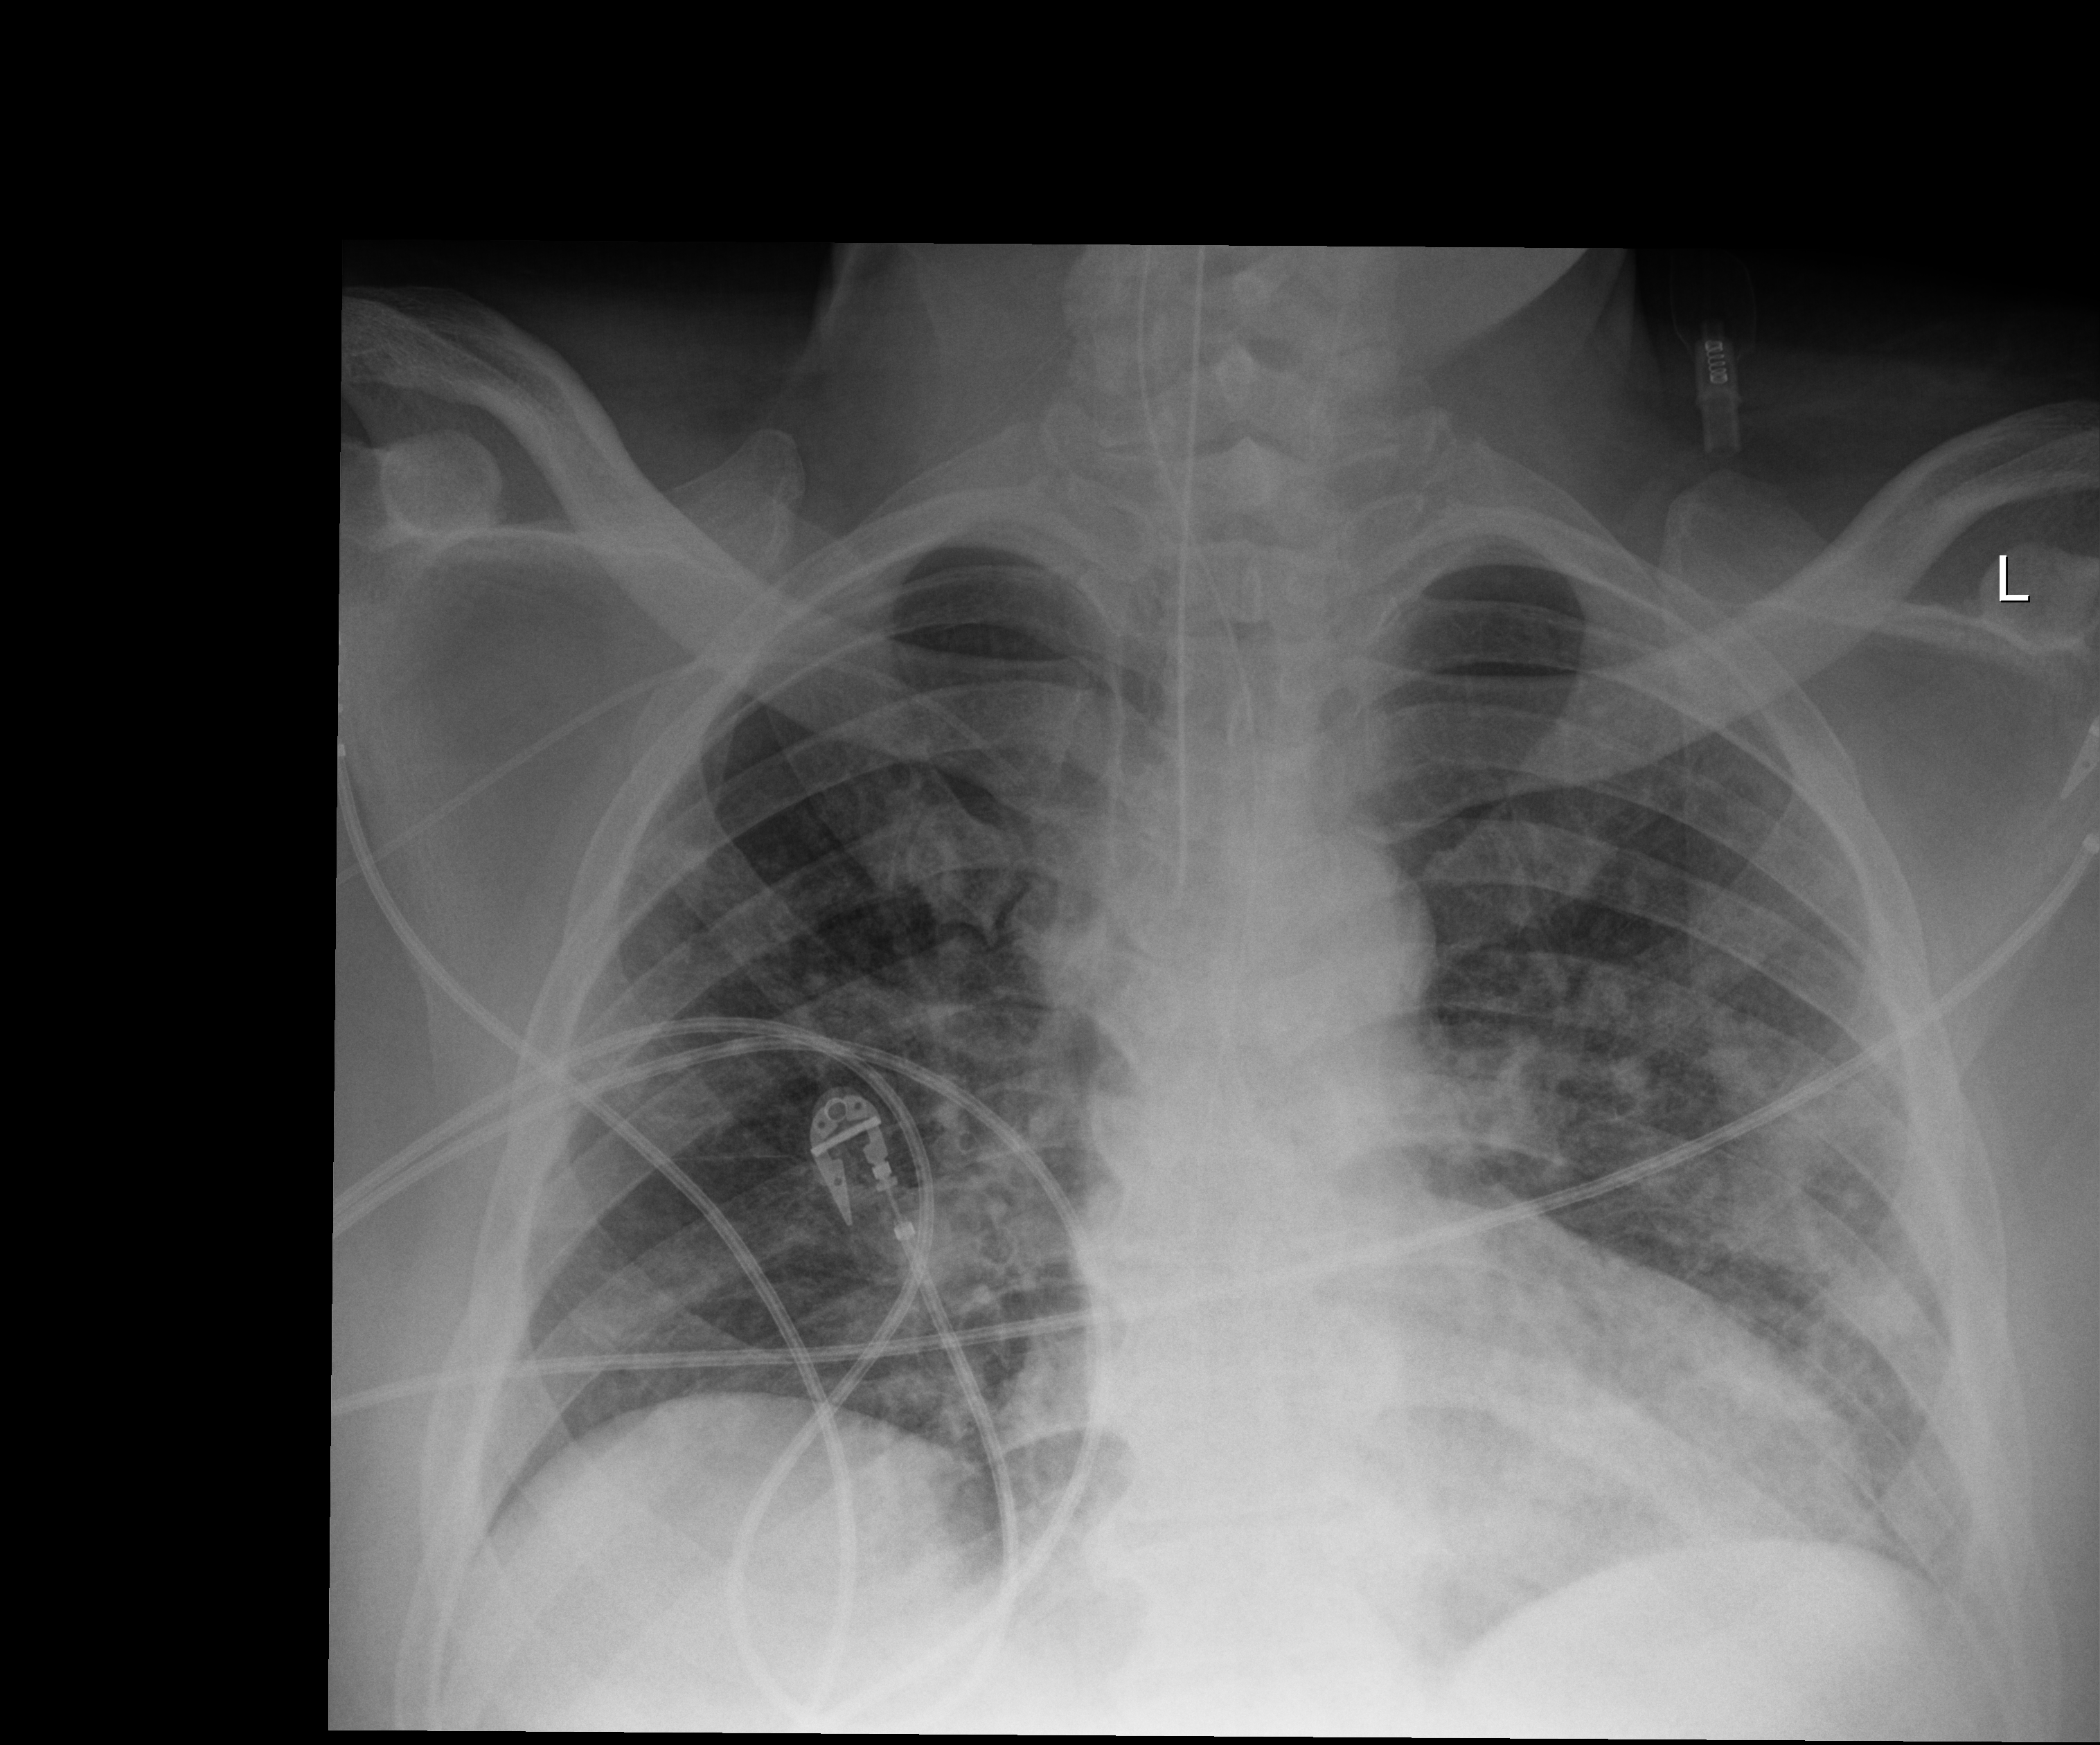
Chest radiograph (digital radiography), anteroposterior (AP) projection. Male patient hospitalised with COVID-19, age 18–59 years.
From the hospital-stay record, not from the radiograph (when in the stay this image was taken is not recorded): mechanically ventilated during this hospital stay: yes; admitted to intensive care during this hospital stay: yes.